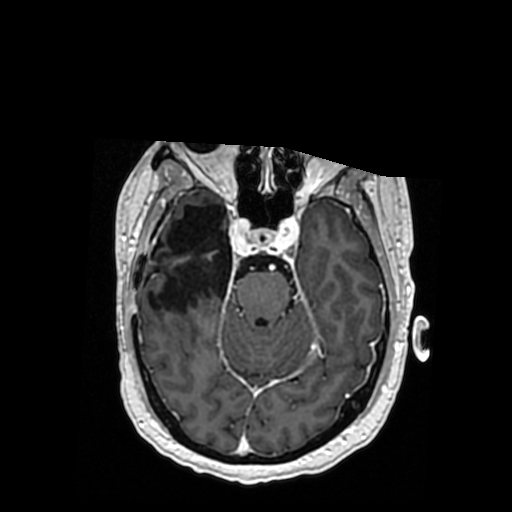
Brain MRI from a brain-tumour surgery series, one axial slice; slice 230 of 364 in the series (ordered by position); T1-weighted post-contrast; 0.5 mm slice thickness; 512 × 512 image matrix, field of view 260 × 260 mm. Case-level facts recorded for this patient, not image findings: histopathology: Oligodendroglioma; WHO grade: 3; IDH mutation: yes.
Outlined on this slice (expert manual segmentation):
- previous resection cavity: bounding box (x1, y1, x2, y2) in pixels: (148, 205, 232, 313)